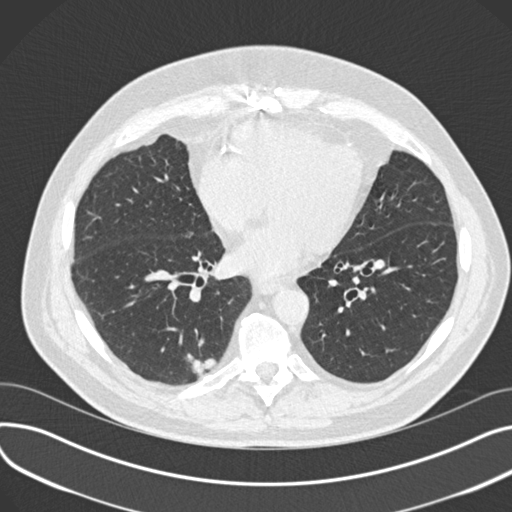
Axial slice from a low-dose chest CT screening exam. Third screening round (two years after baseline). Lung window (W 1500 / L -600 HU). Standard (soft-tissue) reconstruction kernel (B30f). 120 kVp. Slice 104 of 177 in the series. Male, age 68 years at enrolment.
Lesion marked by an expert reader, bounding box <176,346,219,385> (left, top, right, bottom; pixels). The screening reader recorded 4 non-calcified nodules or masses ≥4 mm on this exam (left upper lobe, lingula, right upper lobe, right lower lobe); which of them this box marks is not recorded. Later outcome: lung cancer diagnosed 68 days after this screen — adenosquamous carcinoma, right lower lobe, moderately differentiated (G2), stage IB (AJCC 6th edition), 31 mm at pathology.